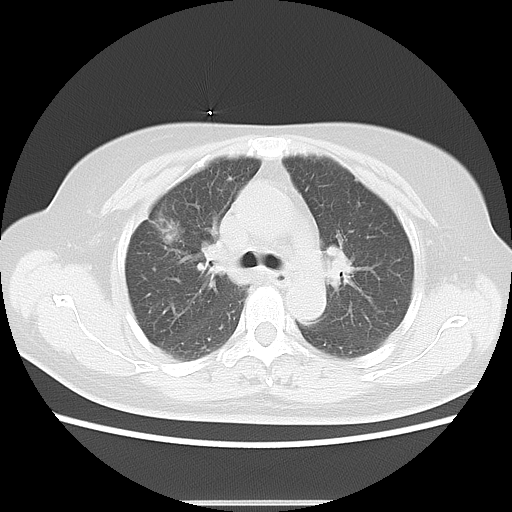
Chest CT, one axial slice; position 9 of 15 along the scan axis; reconstruction kernel LUNG; 120 kVp; lung window (W 1500 / L -600 HU); 5 mm slice thickness; 512 × 512 image matrix, field of view 350 × 350 mm. Female patient, age 57 years. From the clinical record (not read from this slice): clinical TNM (as recorded): T1c N1 M0.
Outlined on this slice (rectangle marked by the reading radiologist):
- lung tumour (recorded histology: adenocarcinoma): box from (x=152, y=215) to (x=189, y=252) px